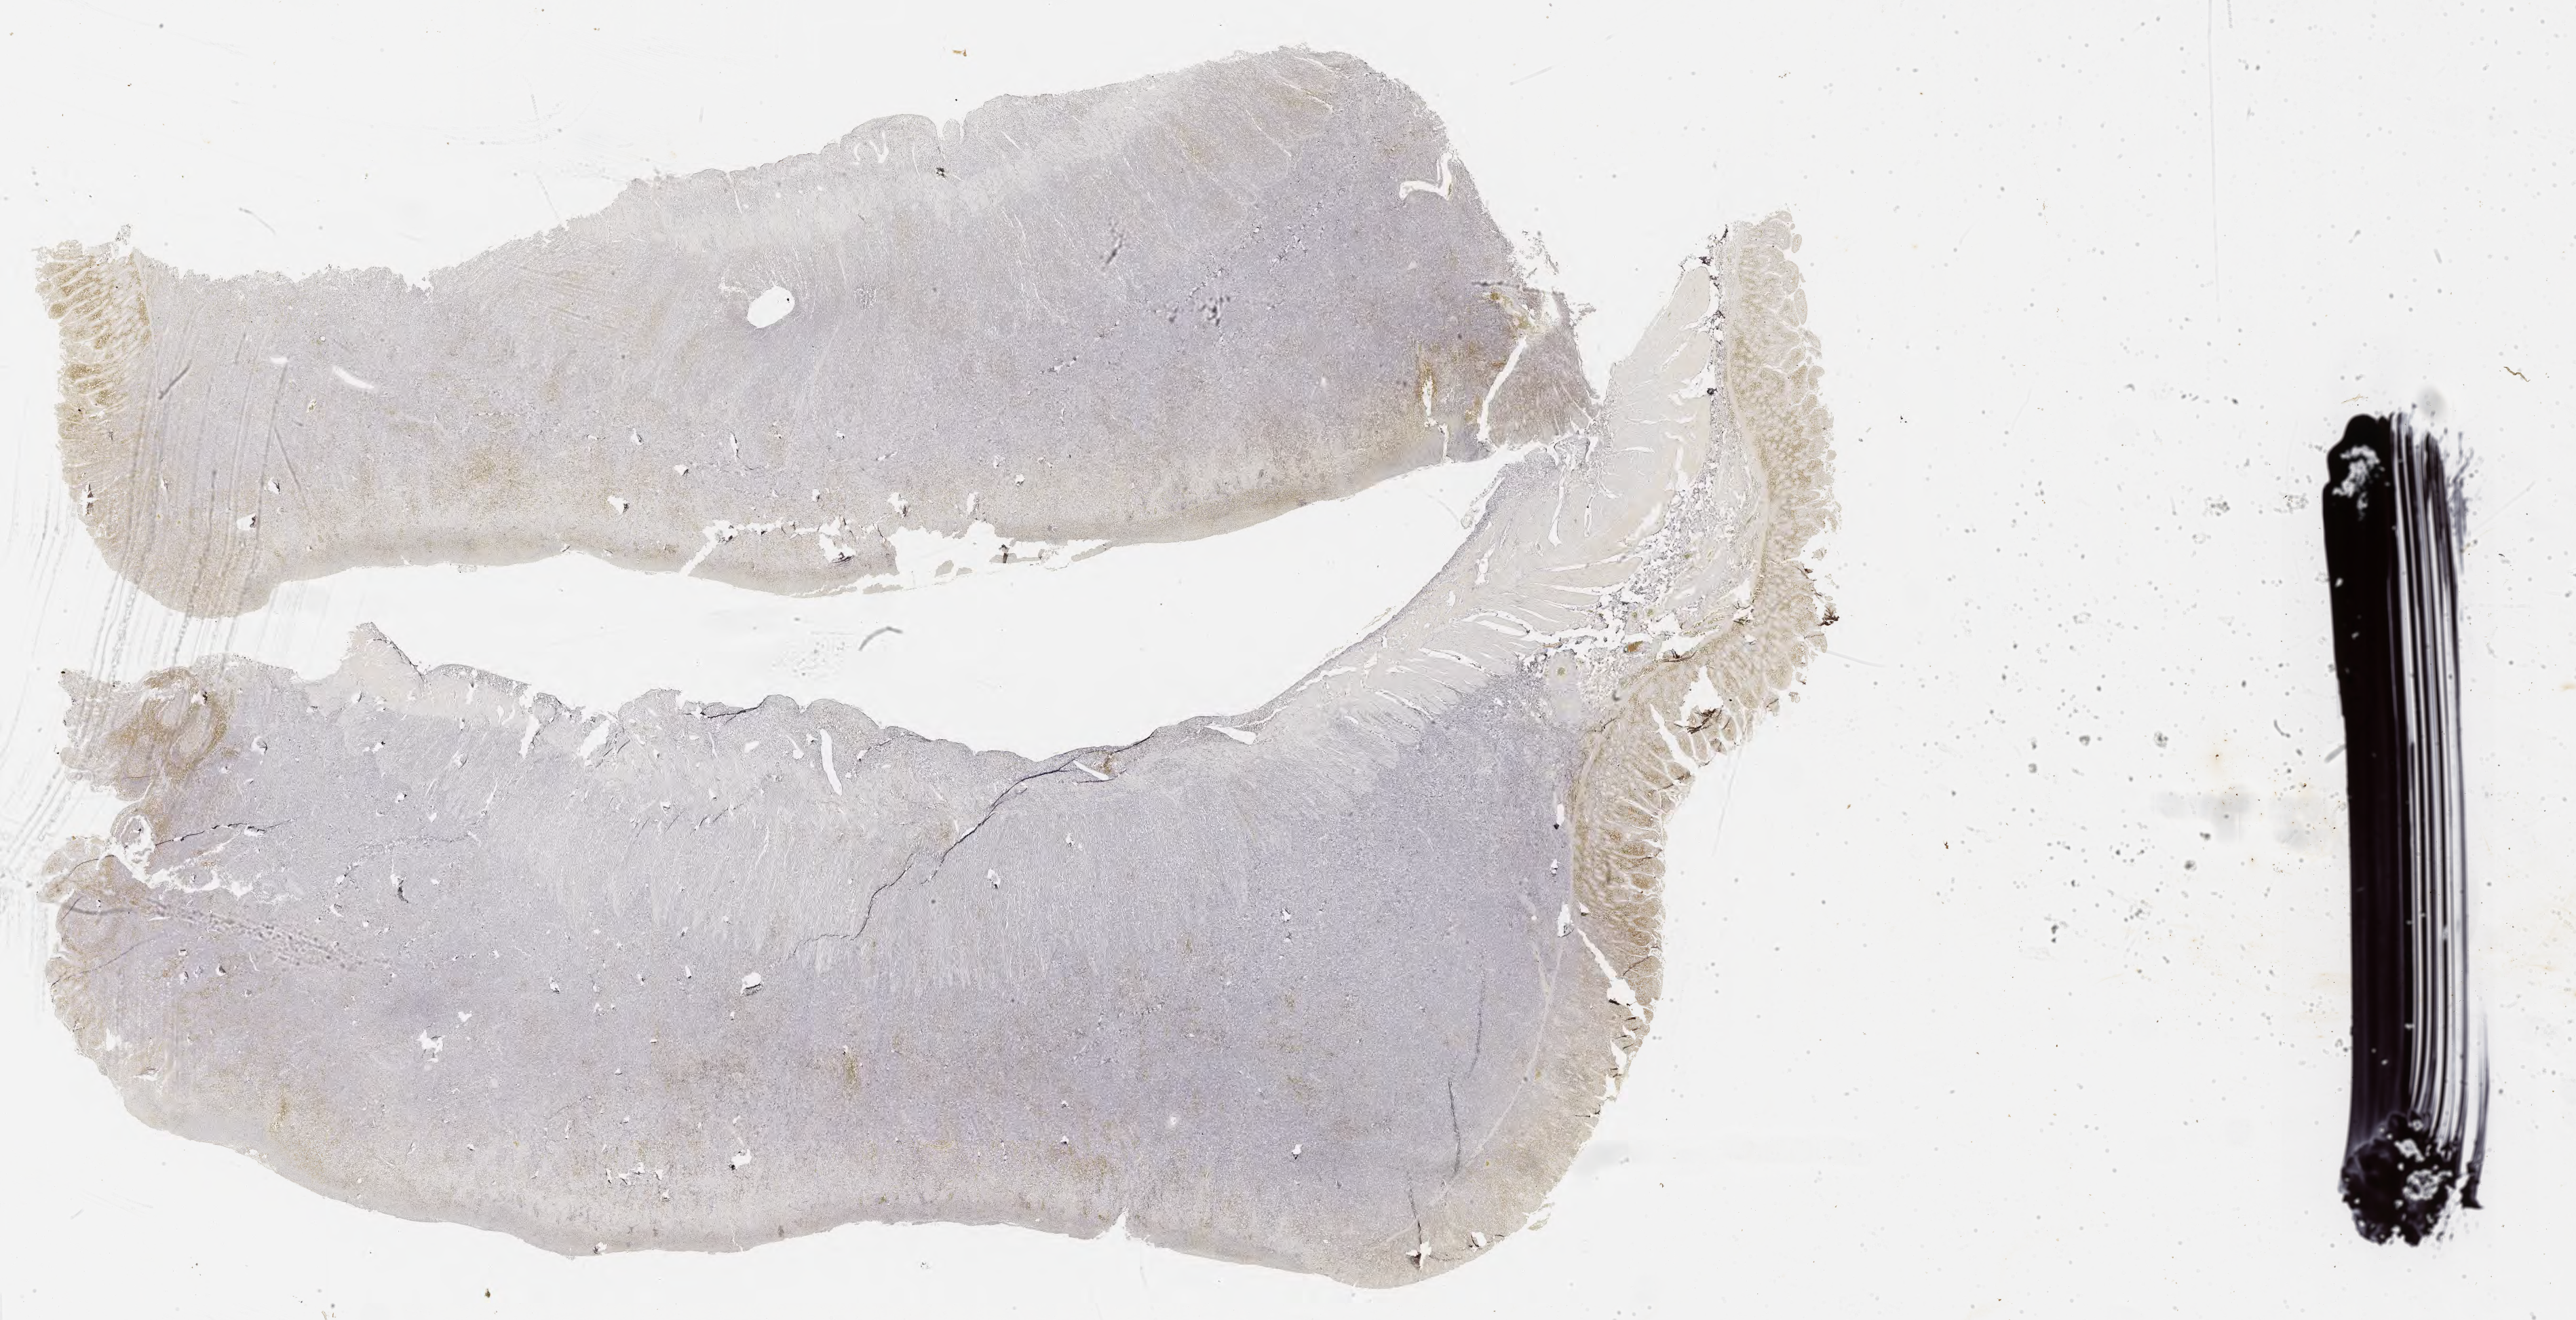
IHC for CD5, whole-slide image, shown as a low-resolution overview of the whole scanned area (about 30.7 x 15.7 mm), specimen: tumor tissue. Female patient, aged 27.
Diagnosis: Burkitt lymphoma, NOS.